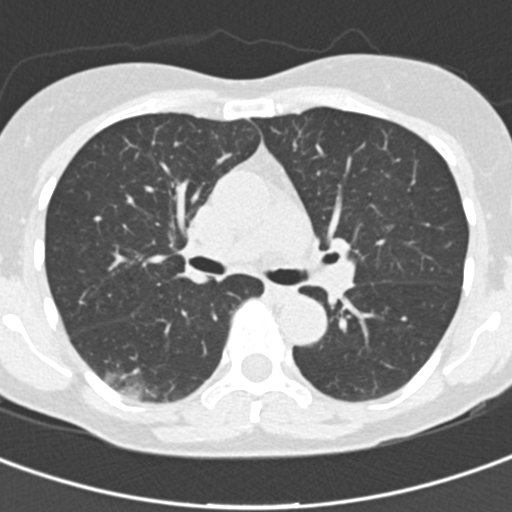
Chest CT (low-dose screening protocol), one axial image, first (baseline) screen, lung window (W 1500 / L -600 HU), 2 mm slice thickness, standard (soft-tissue) reconstruction kernel (B30f), slice 69 of 162 in the series. Female, age 64 years at enrolment. Current smoker at enrolment.
Lesion marked by an expert reader, box from (x=81, y=347) to (x=173, y=413) px. Screening reader's record for this exam (one nodule recorded; not confirmed to be the boxed lesion): non-calcified nodule or mass ≥4 mm, right lower lobe, 31 × 15 mm, poorly defined margins, ground glass attenuation. Participant outcome: lung cancer diagnosed 91 days after this screen — bronchiolo-alveolar carcinoma, non-mucinous, right lower lobe, well differentiated (G1), stage IA (AJCC 6th edition), 20 mm at pathology.